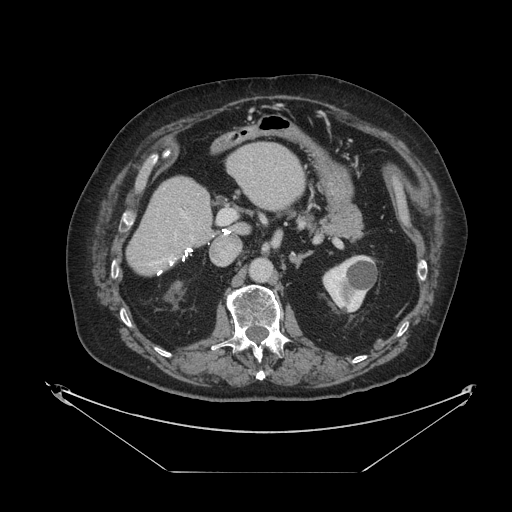
Contrast-enhanced abdominal CT, one axial slice. Position 50 of 121 along the scan axis. Reconstruction kernel STANDARD. 120 kVp. Intravenous contrast given. Soft-tissue window (W 400 / L 40 HU). 2.5 mm slice thickness. 512 × 512 image matrix. Male patient, age 68 years. Case-level facts recorded for this patient, not image findings: diagnosis: colorectal cancer liver metastases, imaged before liver resection; multiple liver metastases: no; largest metastasis: 4 cm; disease in both lobes: no.
Outlined on this slice (outlined manually by an expert reader):
- hepatic veins: bounding box (x1, y1, x2, y2) in pixels: (168, 235, 177, 262)
- liver: (128, 144, 305, 274)
- planned liver remnant (the part of the liver to remain after resection): (128, 143, 305, 274)
- portal vein (with intrahepatic branches): (181, 209, 236, 240)